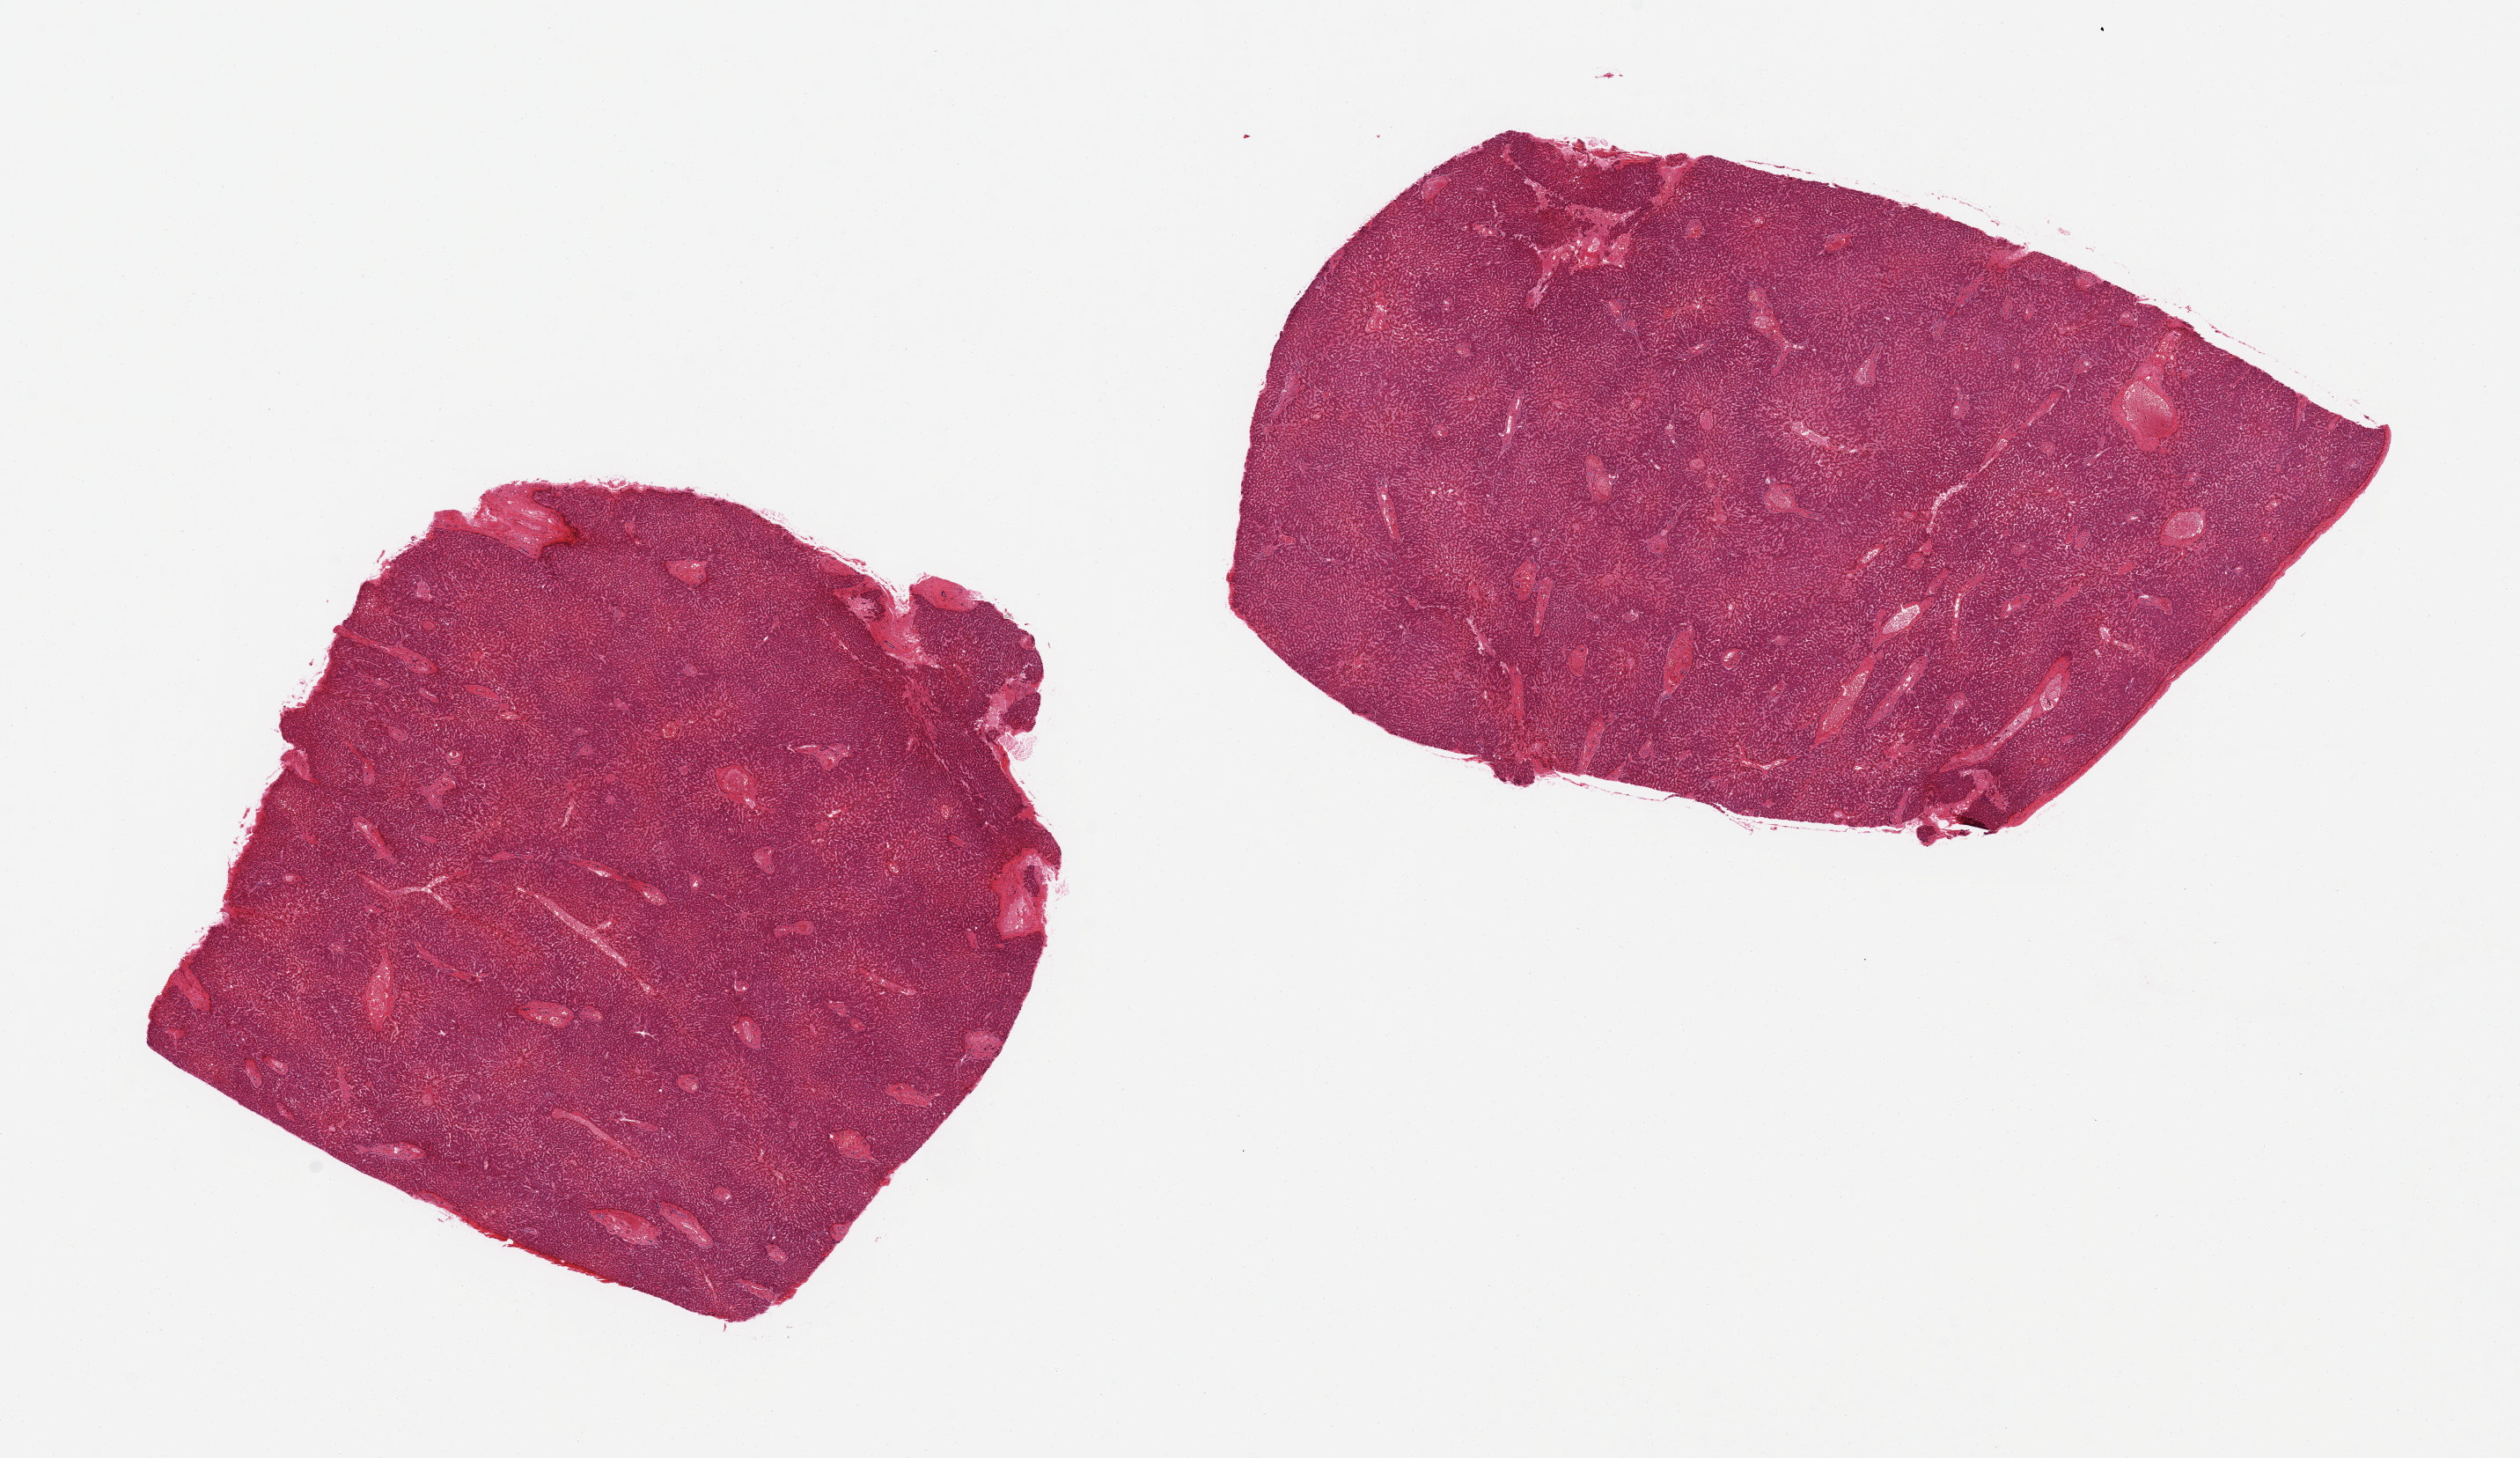
Digitized haematoxylin and eosin-stained section, brightfield, shown as a low-resolution overview of the whole scanned area (about 22.6 x 13.1 mm), PAXgene-fixed paraffin-embedded (PFPE) section, sampled site (target tissue): liver, donor tissue sample. Donor sex: male.
Review note (as recorded): 2 pieces, moderate congestion; no significant steatosis.